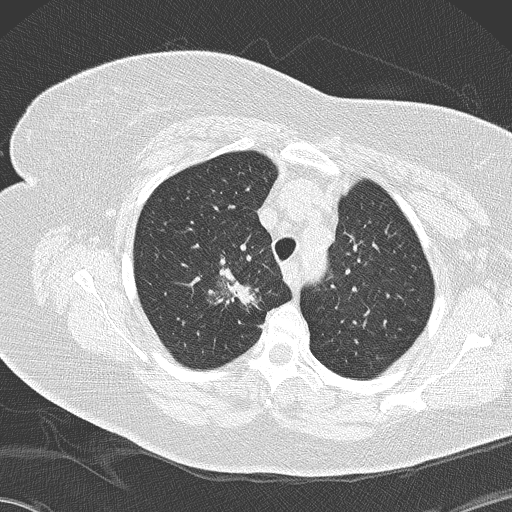
Chest CT (low-dose screening protocol), one axial image, second annual screen, lung window (W 1500 / L -600 HU), lung (sharp) reconstruction kernel (B50f), slice 33 of 146 in the series. Female, age 72 years at enrolment. Former smoker at enrolment.
Expert reader's lesion annotation, bounding box <179,241,264,328> (left, top, right, bottom; pixels). The screening reader recorded 4 non-calcified nodules or masses ≥4 mm on this exam (right lower lobe, right lower lobe, right lower lobe, right upper lobe); which of them this box marks is not recorded. Official screen result: positive, other. Participant outcome: lung cancer diagnosed 52 days after this screen — bronchiolo-alveolar adenocarcinoma, NOS, right upper lobe, stage IIIB (AJCC 6th edition), 45 mm at pathology.